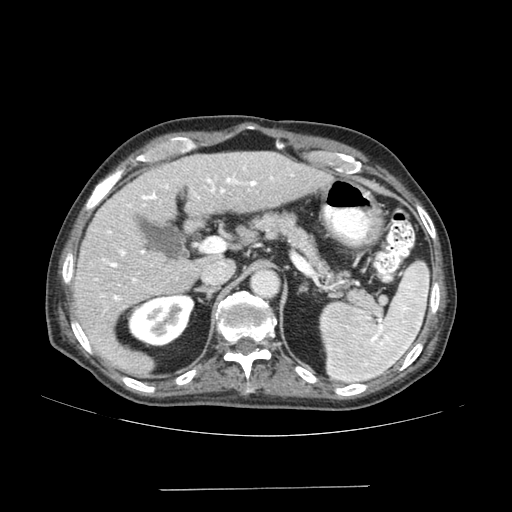
Contrast-enhanced abdominal CT (liver protocol), one axial slice. Reconstruction kernel SOFT. Soft-tissue window (W 400 / L 40 HU). 2.5 mm slice thickness. 512 × 512 image matrix, field of view 400 × 400 mm. Case-level facts recorded for this patient, not image findings: diagnosis: hepatocellular carcinoma (patient treated with transarterial chemoembolisation; whether this scan precedes or follows treatment is not stated here); TNM stage (as recorded): Stage-IVA; Child-Pugh class: A; tumour differentiation: poorly differentiated.
Structures marked on this image (semi-automatic segmentation, software-assisted and operator-edited):
- liver parenchyma outside the tumour (the mass and vessels are separate outlines, so this box may not span the whole liver): bounding box (x1, y1, x2, y2) in pixels: (74, 152, 331, 376)
- liver vessels: (95, 166, 293, 300)